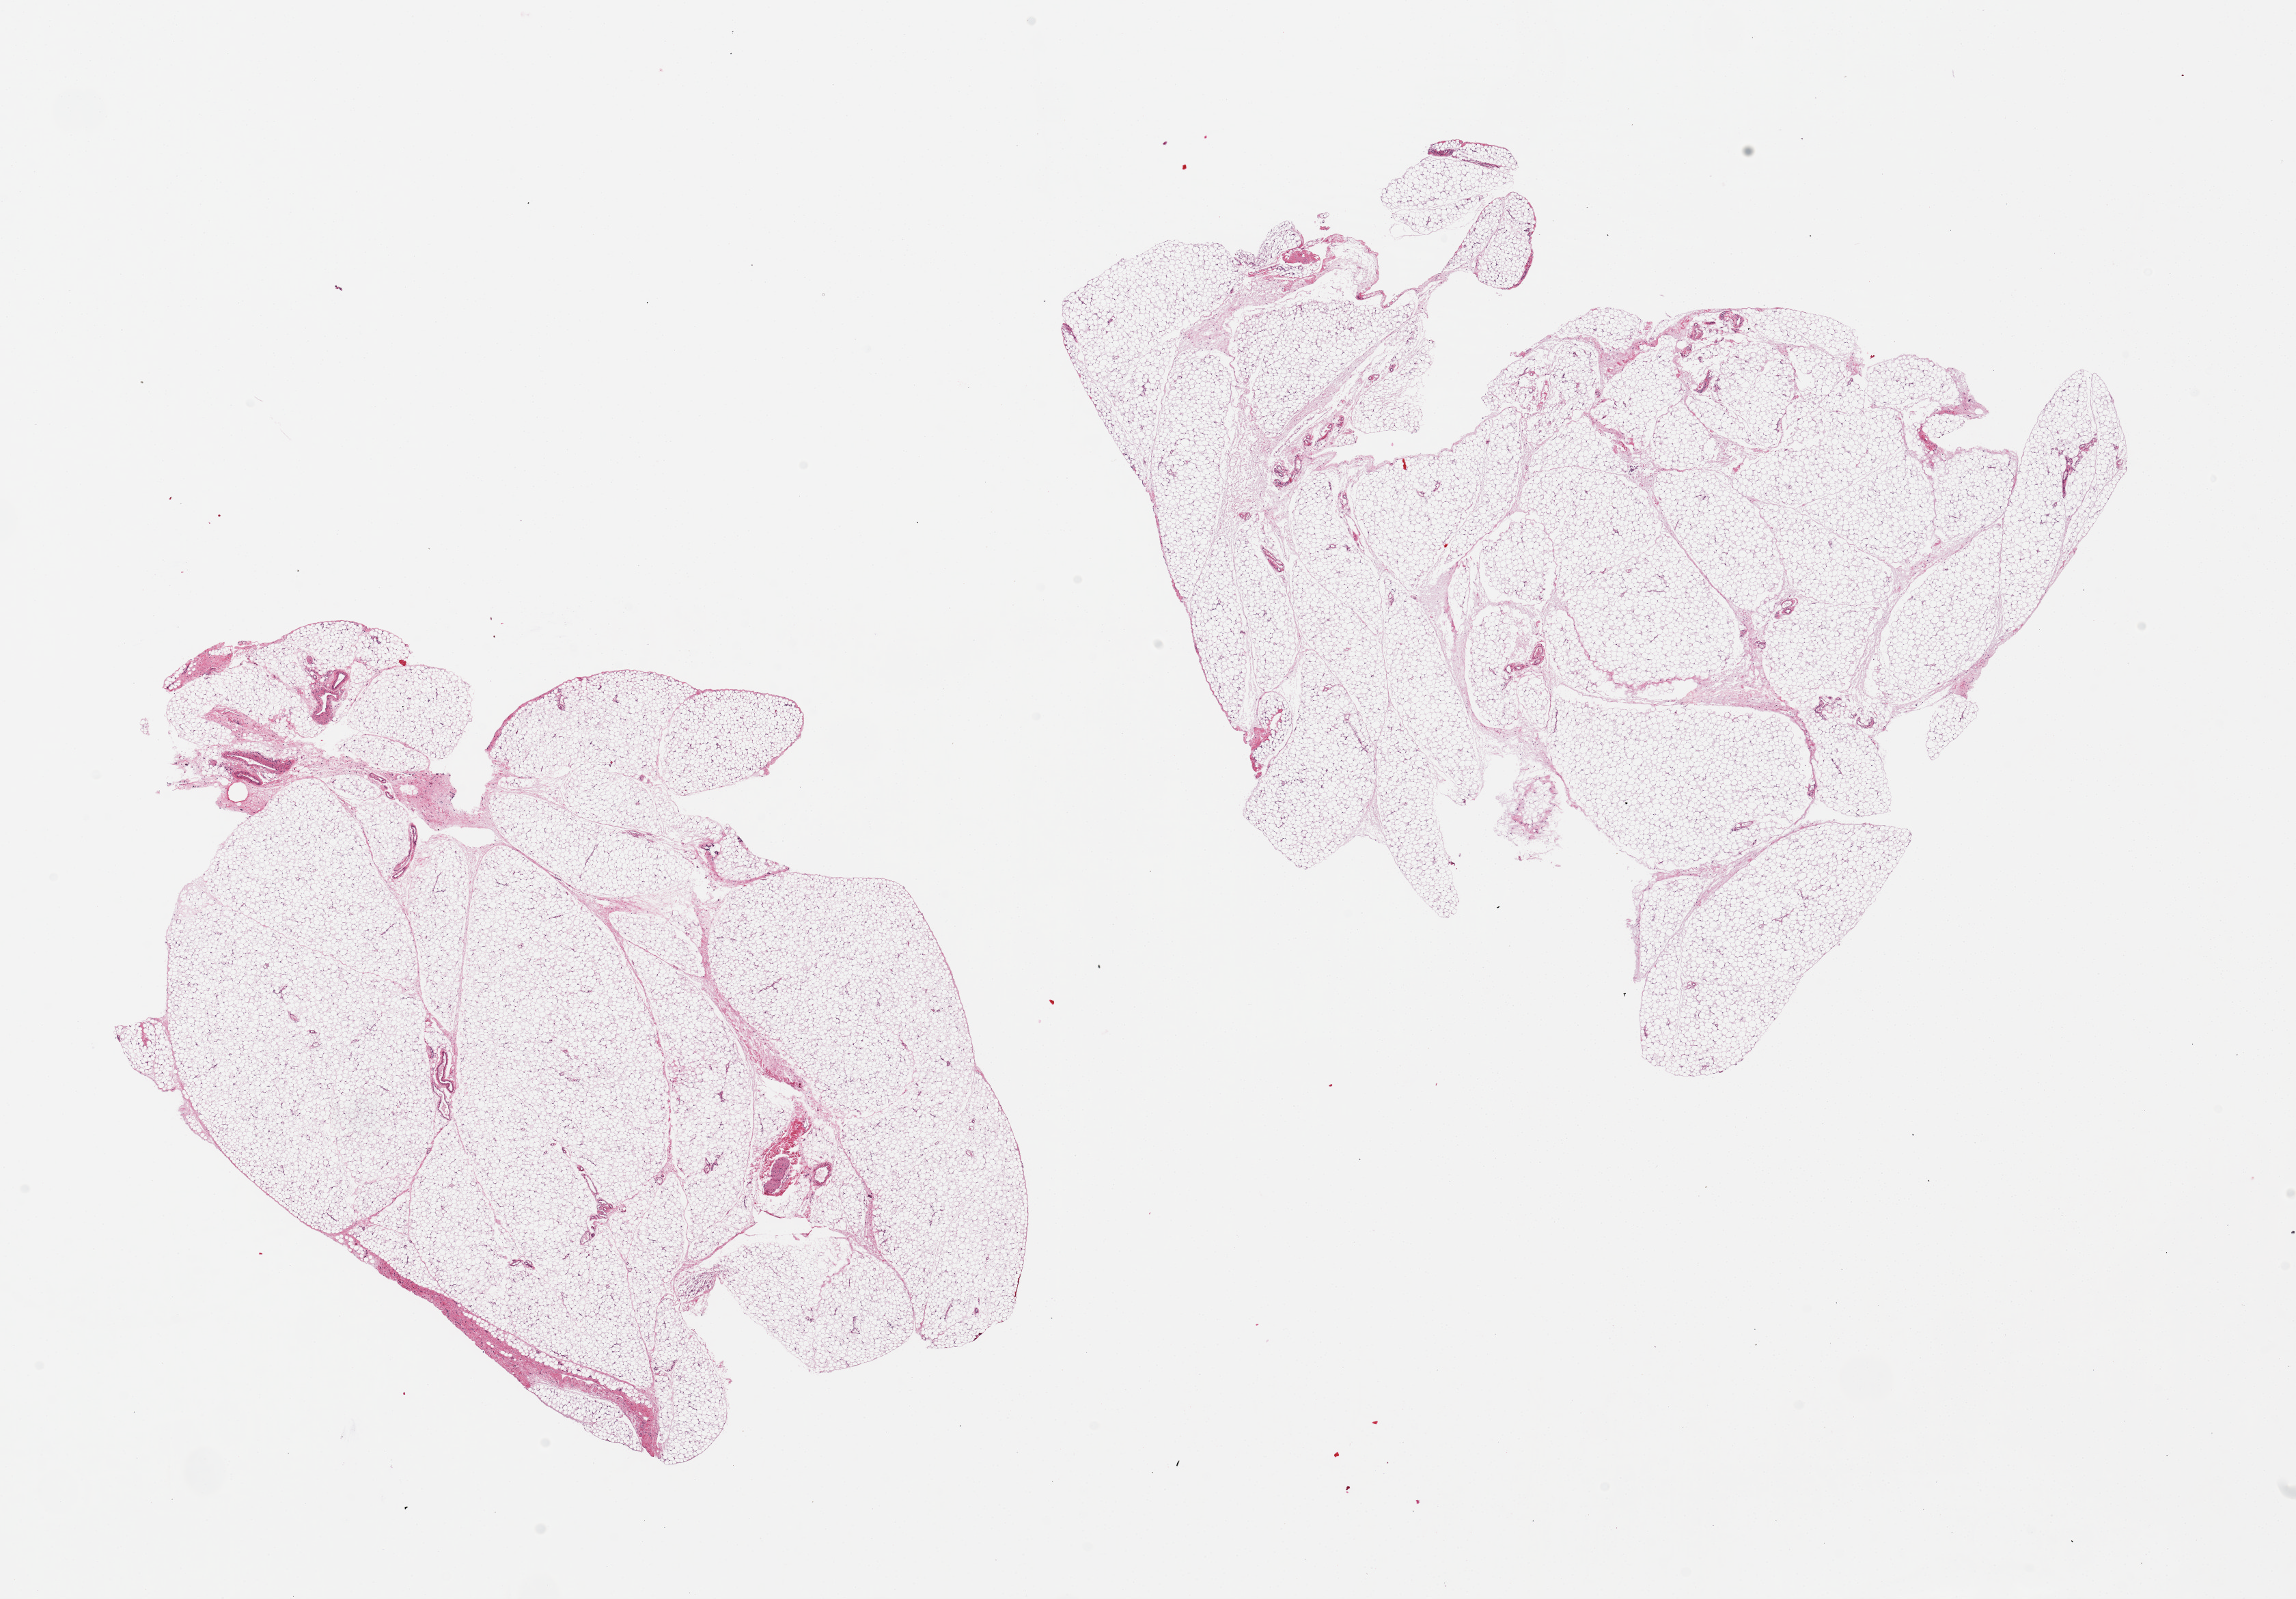
Whole-slide image, H&E stain, shown as a low-resolution overview of the whole scanned area (about 26.6 x 18.5 mm, acquisition: 20x scan), PAXgene-fixed, paraffin-embedded tissue, sampled site (target tissue): omentum, tissue donor sample. Female donor.
Reviewer comment on this tissue sample: 2 pieces, 12x9.5 & 12x8mm; well fixed.